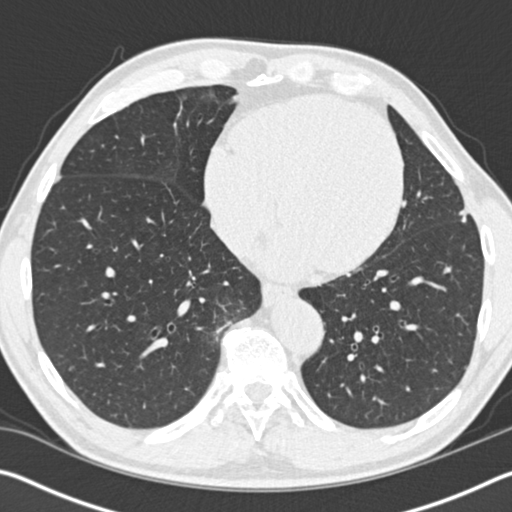
Low-dose screening chest CT, one axial slice. Slice 51 of 162 in the series (ordered by position). 120 kVp. Lung window (W 1500 / L -600 HU). 2 mm slice thickness. 512 × 512 image matrix.
Outlined on this slice (outlined manually by an expert reader):
- lesion 1 (tumor, upper lobe of left lung): bounding box (x1, y1, x2, y2) in pixels: (459, 209, 469, 223)